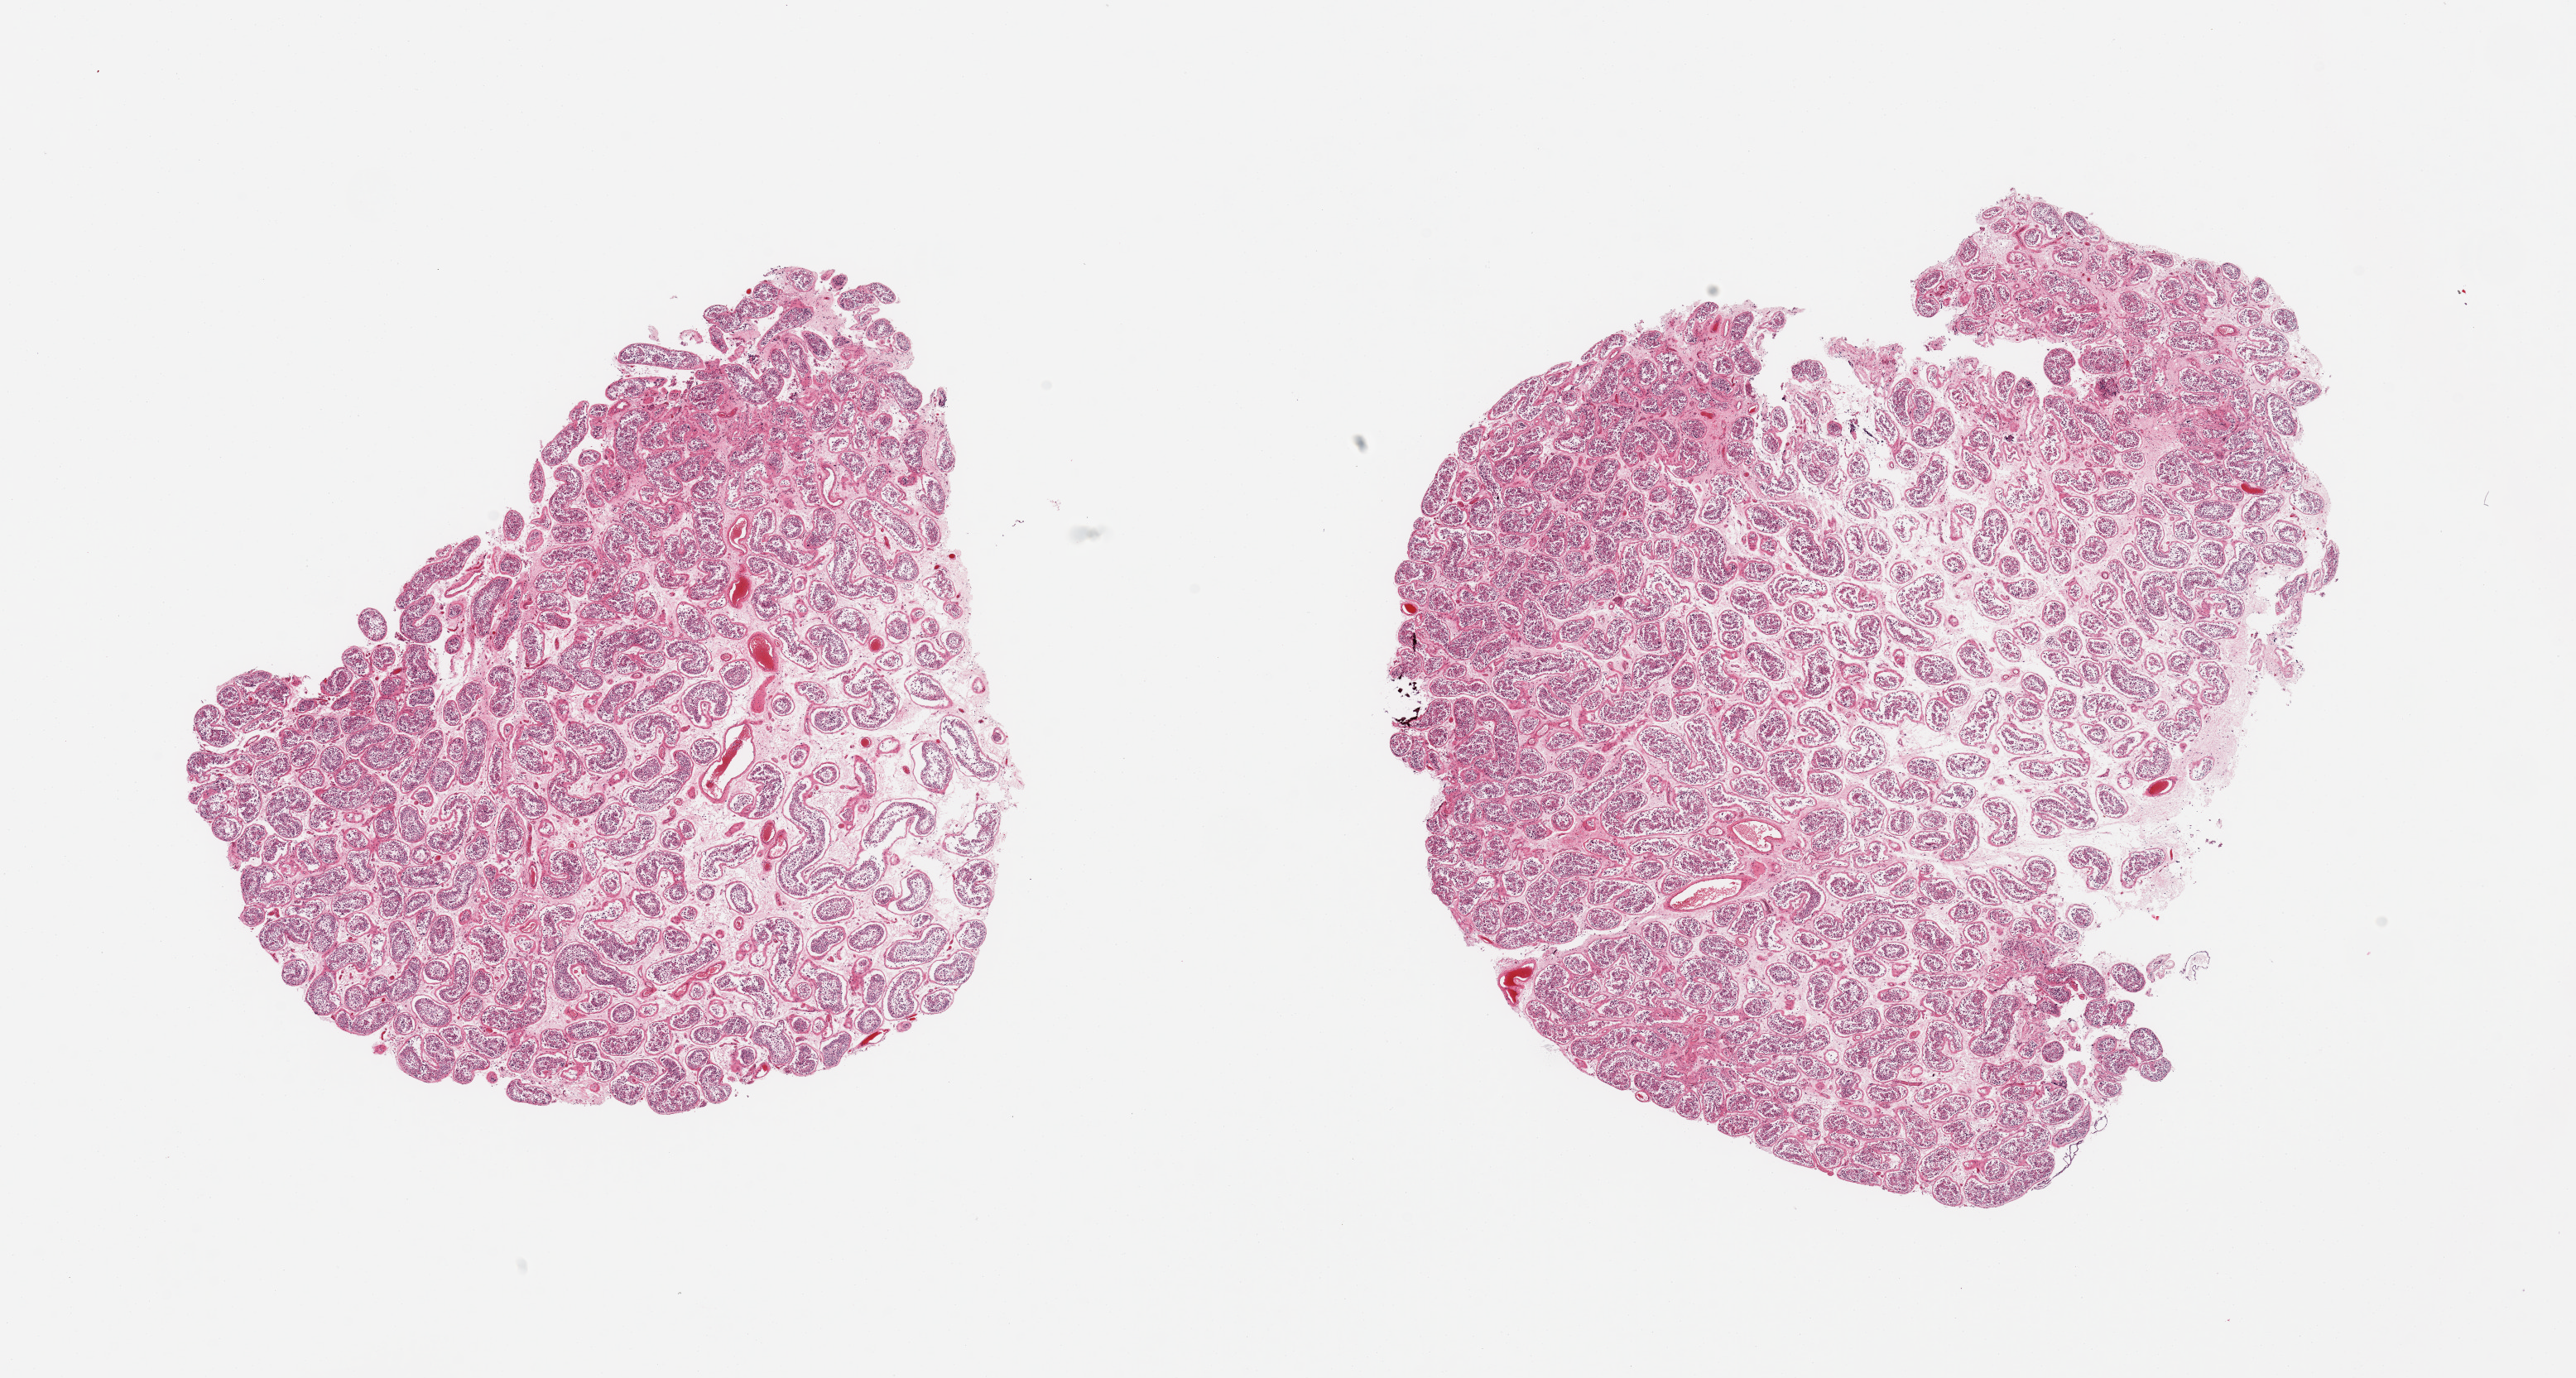
Haematoxylin and eosin whole-slide image, brightfield, a low-resolution overview of the entire scanned area, about 24.6 x 13.2 mm. PAXgene-fixed, paraffin-embedded tissue. Target tissue: testis. Tissue donor sample. Donor: male.
Review note (as recorded): 2 pieces, spermatogenesis appears reduced.